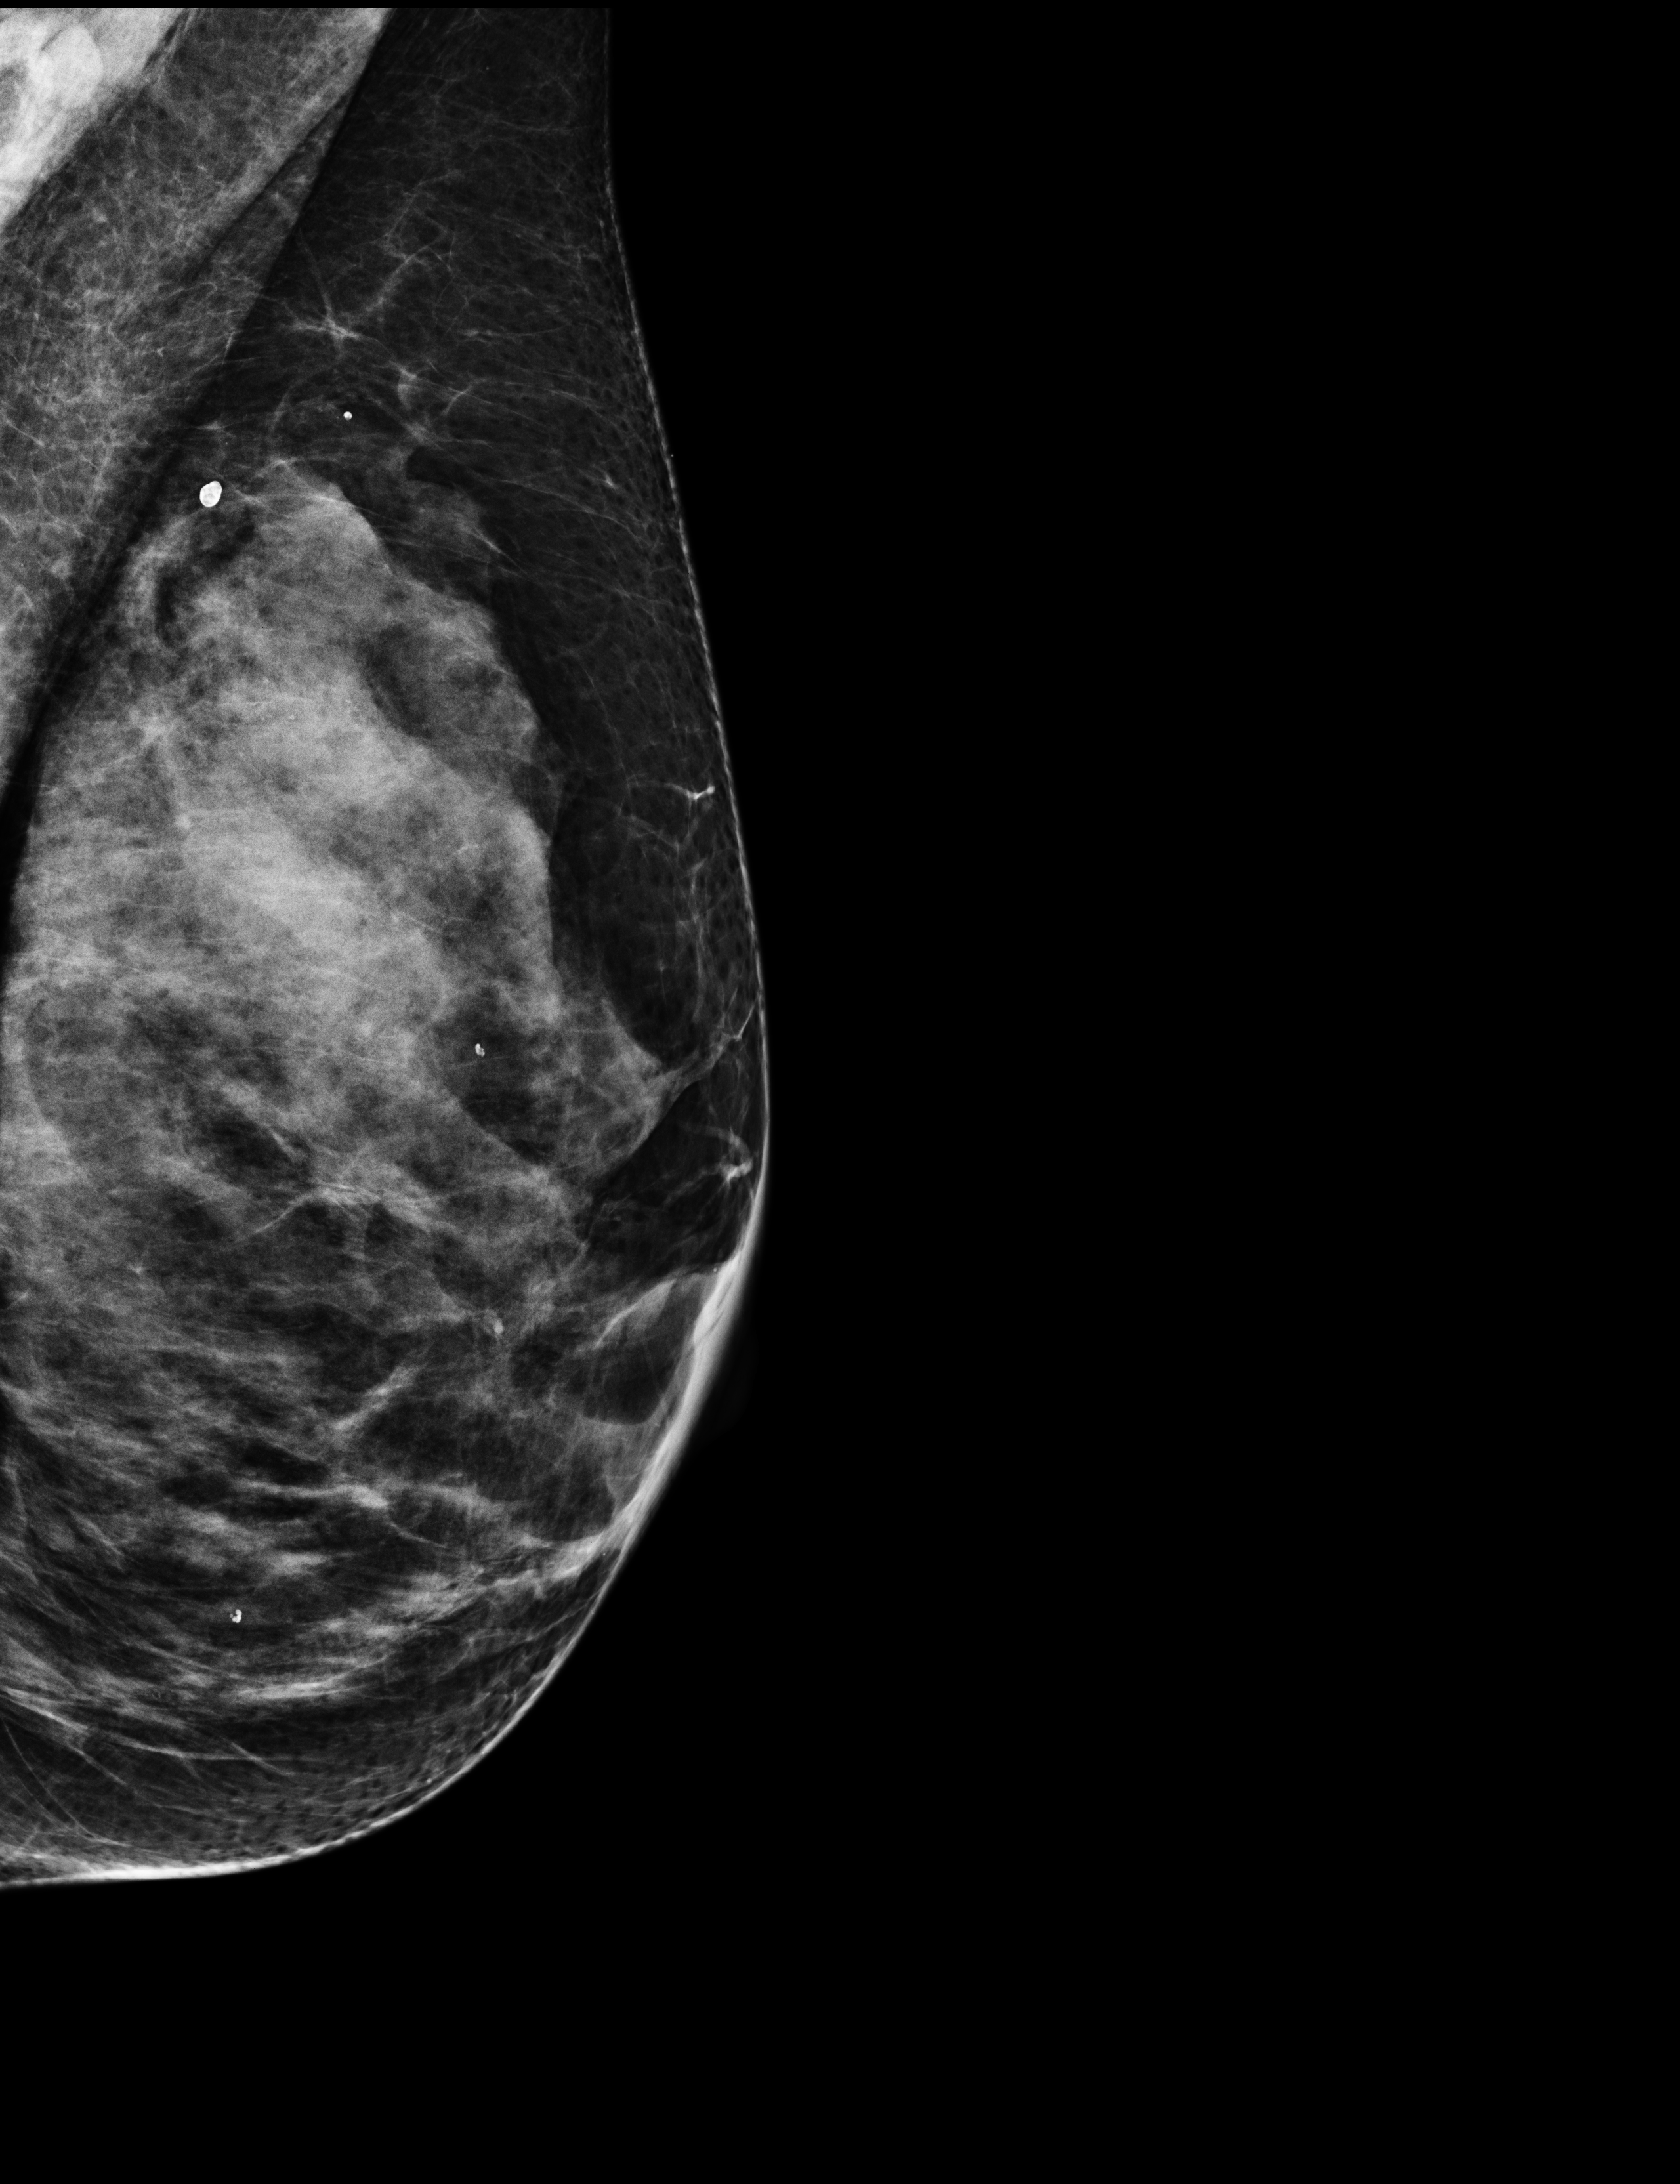
Full-field digital mammogram (FFDM); left breast; medio-lateral oblique projection; screening examination; system: Selenia Dimensions. Female patient, age 64 years.
Final BI-RADS category for the screening round (tomosynthesis exam, both breasts): category 1.